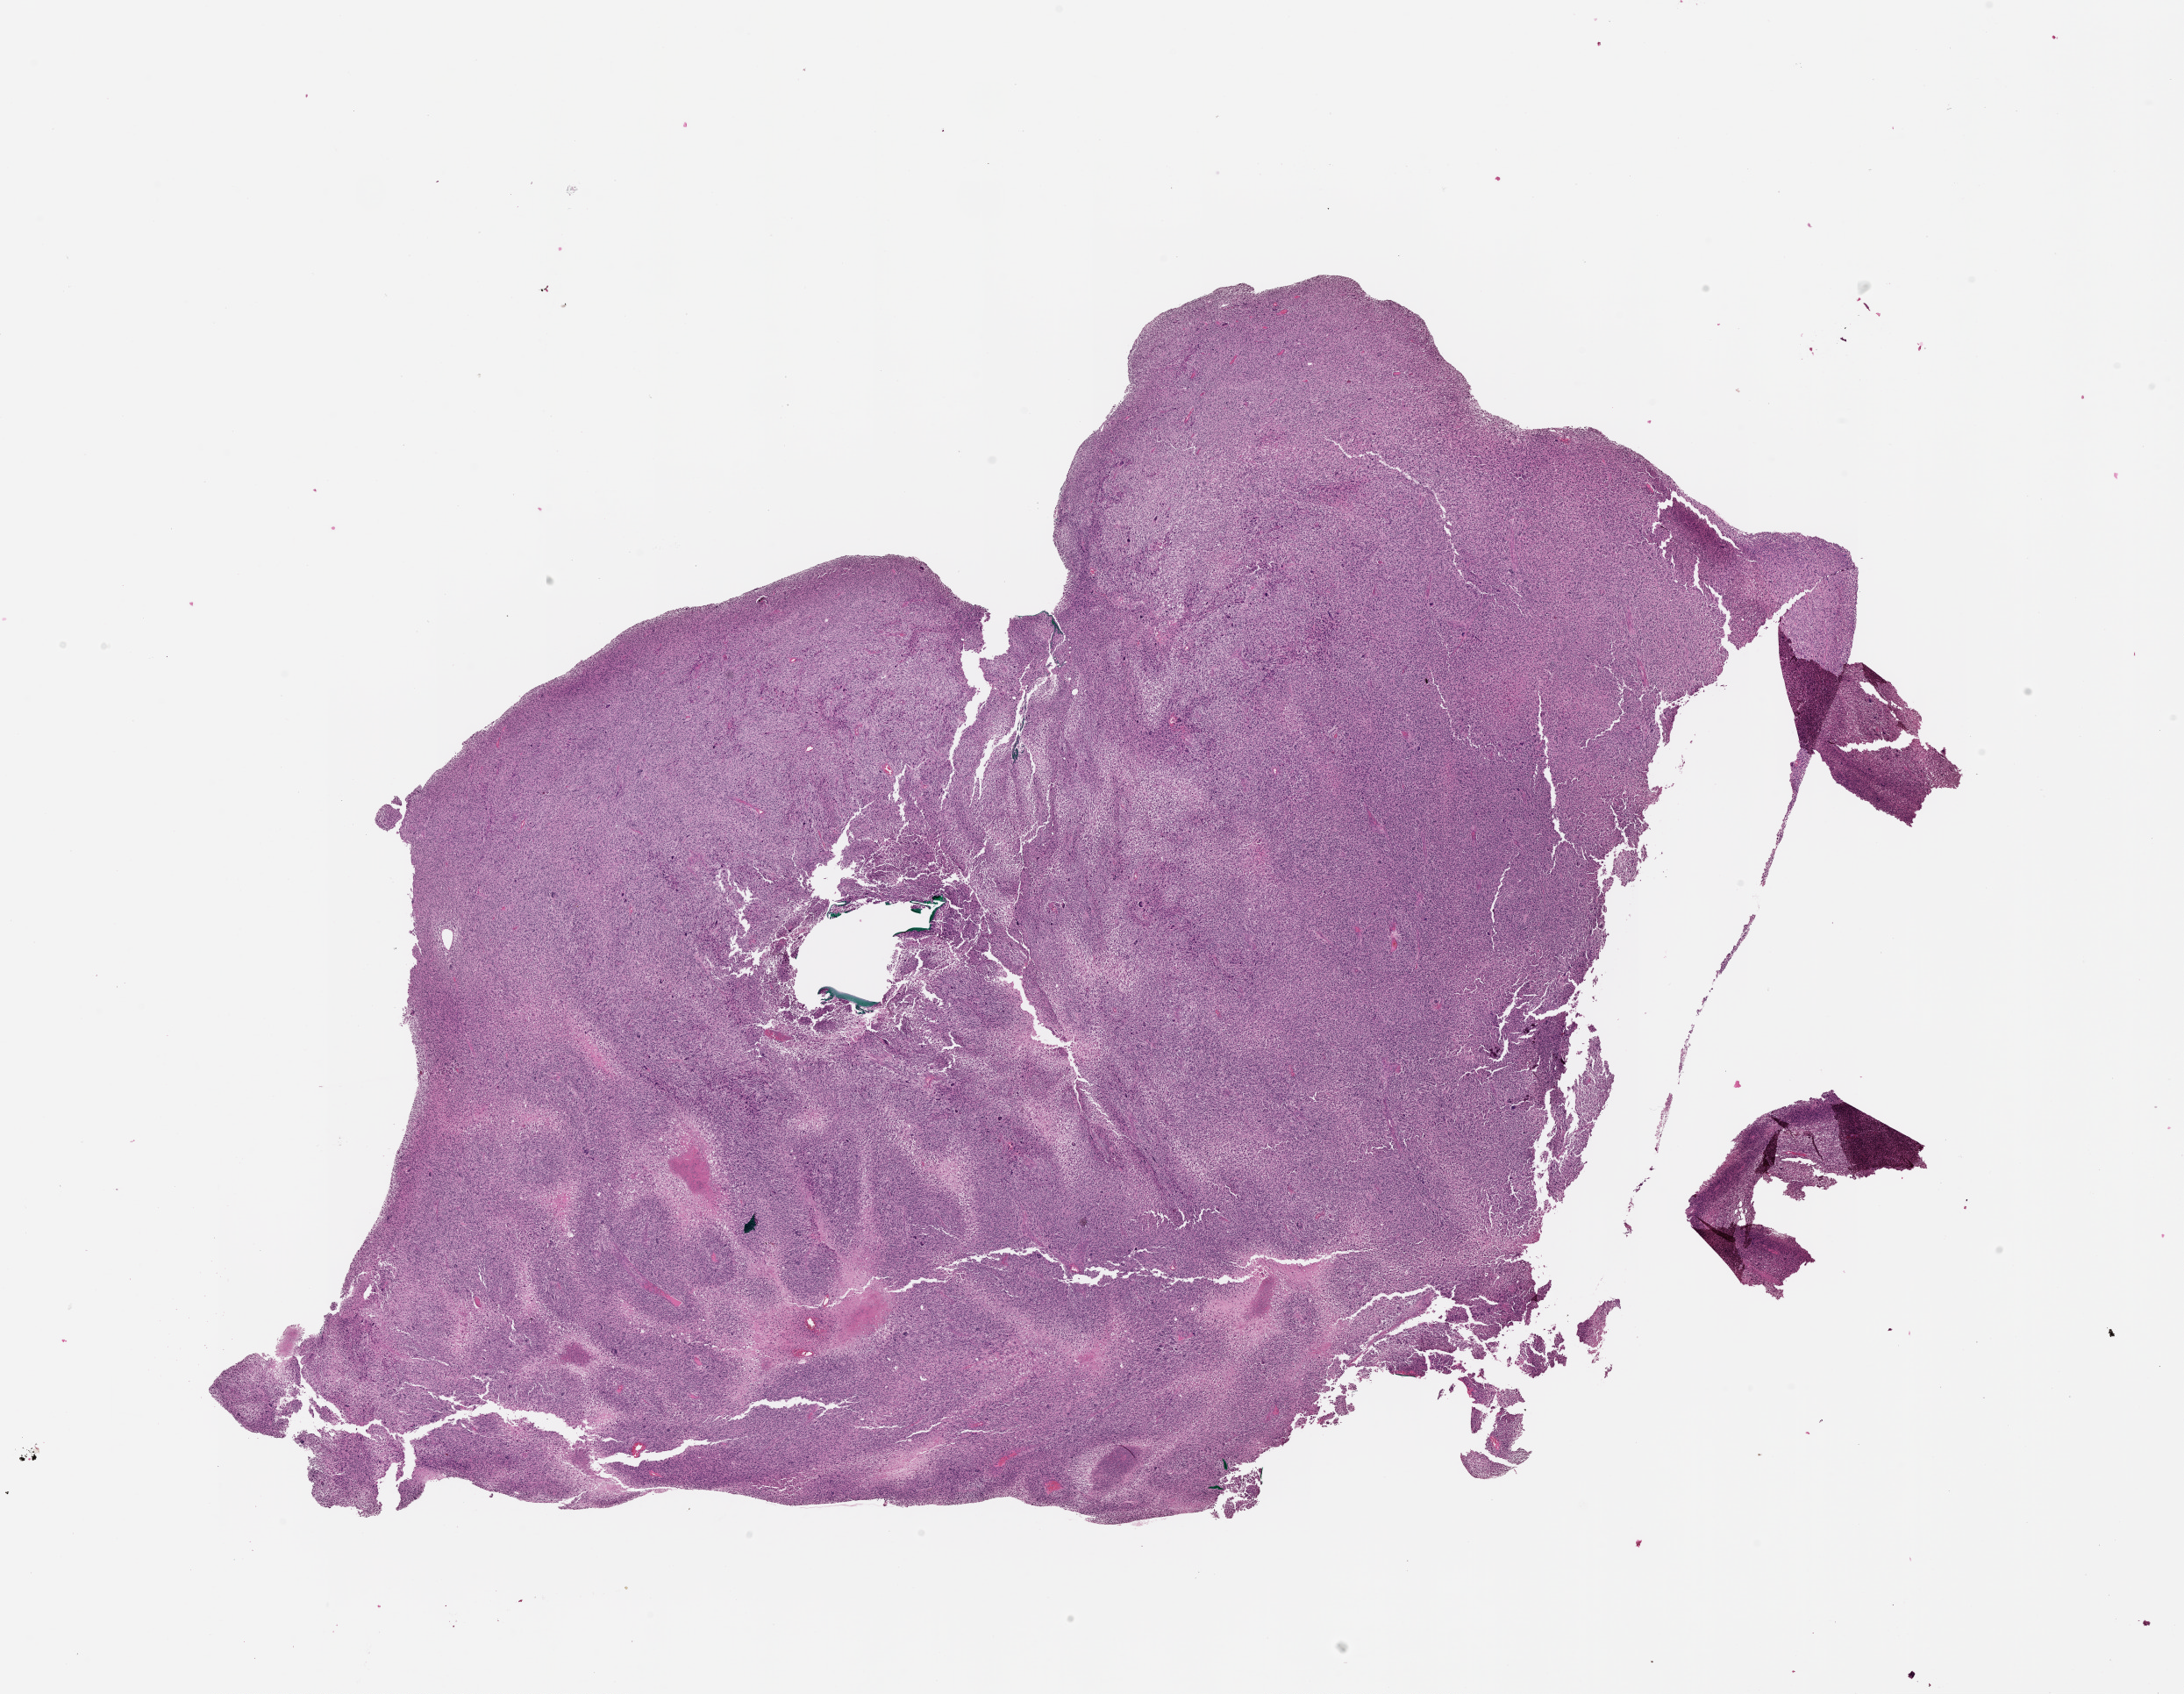
Hematoxylin and eosin (H&E) stained whole-slide image, whole scanned area (about 20.0 x 15.5 mm) shown as a low-resolution overview.
Patient diagnosis (cohort enrolment): sarcoma (site not recorded at cohort level).